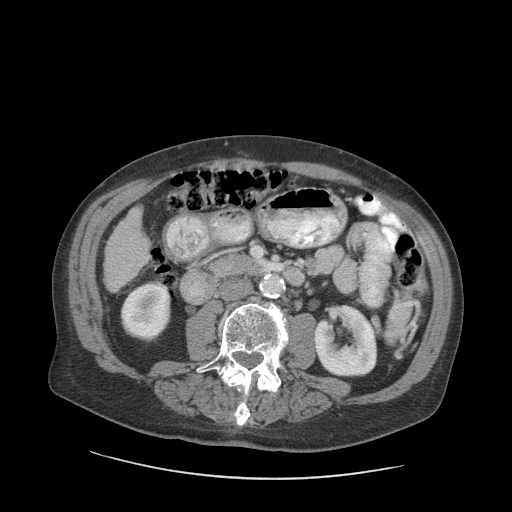
Contrast-enhanced abdominal CT (liver protocol), one axial slice; slice 26 of 89 in the series (ordered by position); reconstruction kernel STANDARD; soft-tissue window (W 400 / L 40 HU); 2.5 mm slice thickness; 512 × 512 image matrix. From the clinical record (not read from this slice): diagnosis: hepatocellular carcinoma (patient treated with transarterial chemoembolisation; whether this scan precedes or follows treatment is not stated here); TNM stage (as recorded): Stage-I; Child-Pugh class: A; tumour nodularity: uninodular.
Outlined on this slice (semi-automatically segmented with operator editing):
- liver parenchyma outside the tumour (the mass and vessels are separate outlines, so this box may not span the whole liver): bounding box [x1, y1, x2, y2] px = [104, 208, 150, 292]
- liver vessels: [129, 265, 131, 267]